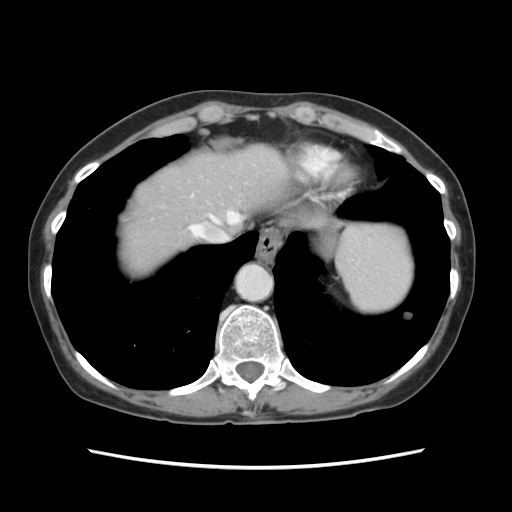
Contrast-enhanced abdominal CT, one axial slice. Position 105 of 120 along the scan axis. Intravenous contrast given. Soft-tissue window (W 400 / L 40 HU). 2.5 mm slice thickness. 512 × 512 image matrix, field of view 330 × 330 mm. Female patient, age 70 years. Case-level facts recorded for this patient, not image findings: diagnosis: colorectal cancer liver metastases, imaged before liver resection; multiple liver metastases: no; largest metastasis: 2.5 cm; chemotherapy before resection: yes.
Outlined on this slice (expert manual segmentation):
- hepatic veins: box from (x=191, y=213) to (x=230, y=242) px
- liver: (x=118, y=146)–(x=289, y=274)
- planned liver remnant (the part of the liver to remain after resection): (x=155, y=146)–(x=288, y=236)